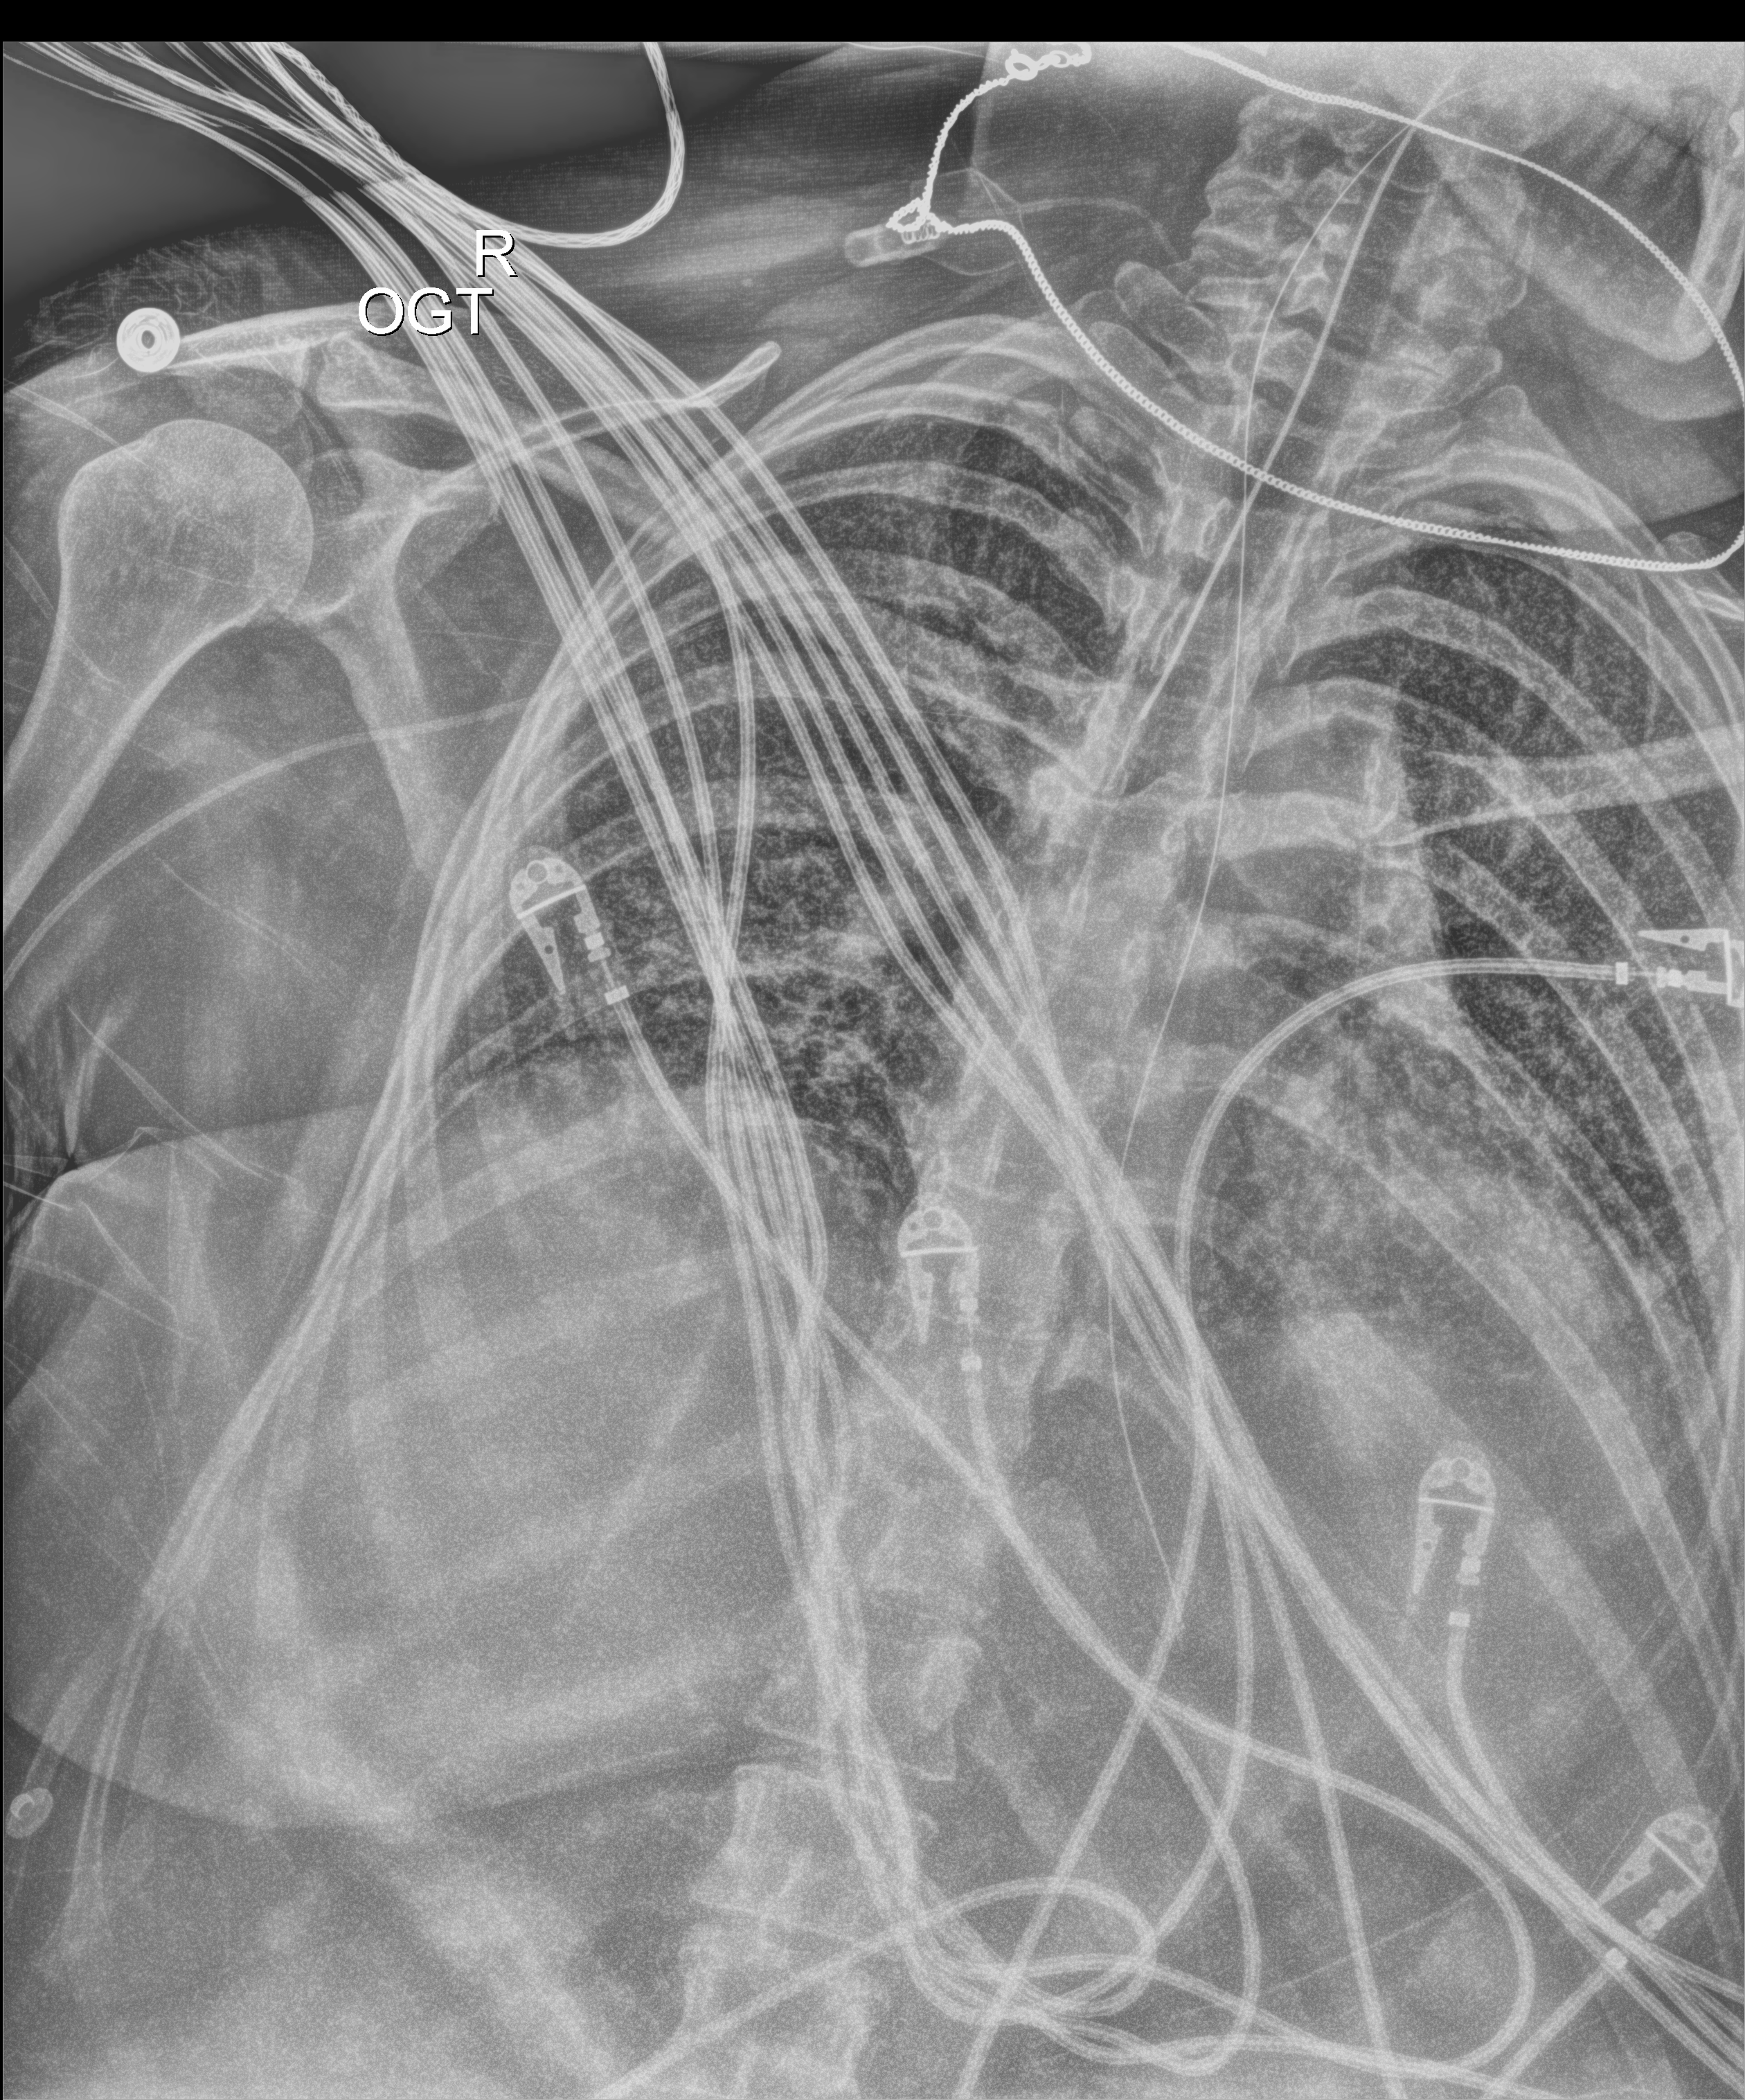
Portable chest radiograph; anteroposterior (AP) projection. Patient hospitalised with COVID-19; female, aged 18–59 years.
From the hospital-stay record, not from the radiograph (when in the stay this image was taken is not recorded): mechanically ventilated during this hospital stay: yes; admitted to intensive care during this hospital stay: yes.